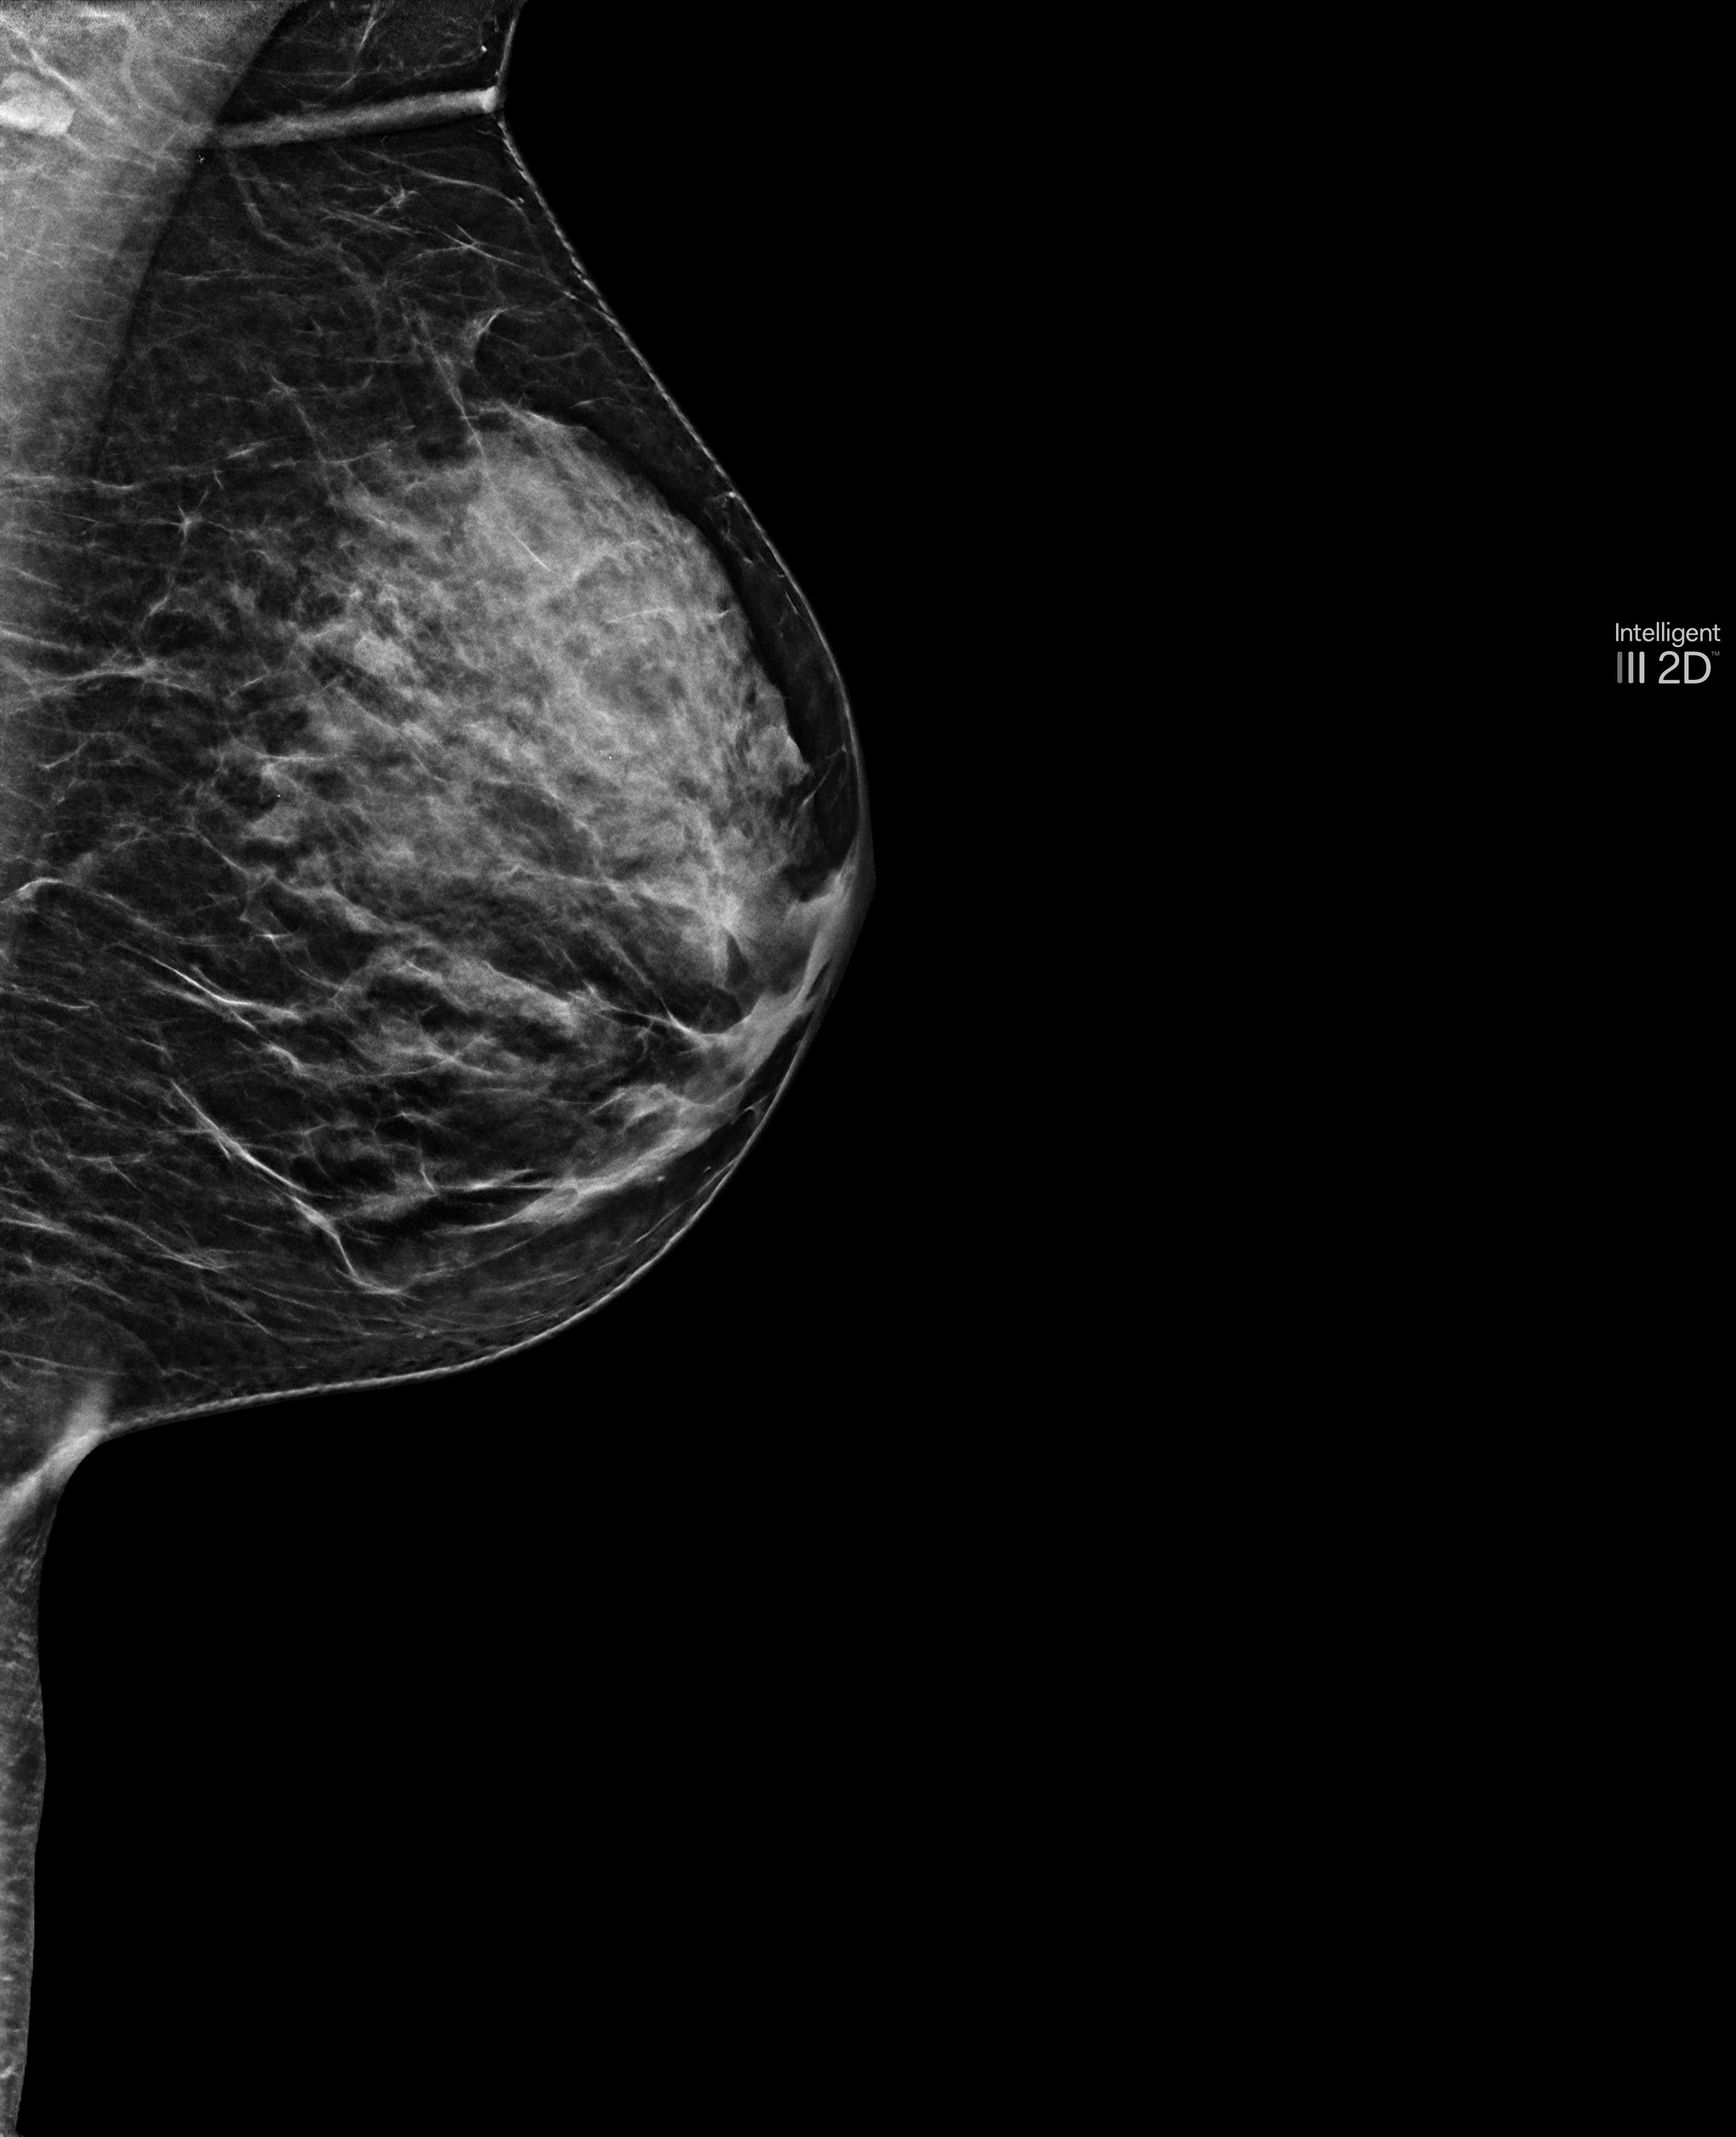
Annual screening mammography examination; compressed breast thickness 47 mm. Patient aged 51 years (female).
Image type: synthesized 2-D view from tomosynthesis. Breast: left. Projection: mediolateral oblique (MLO) view.